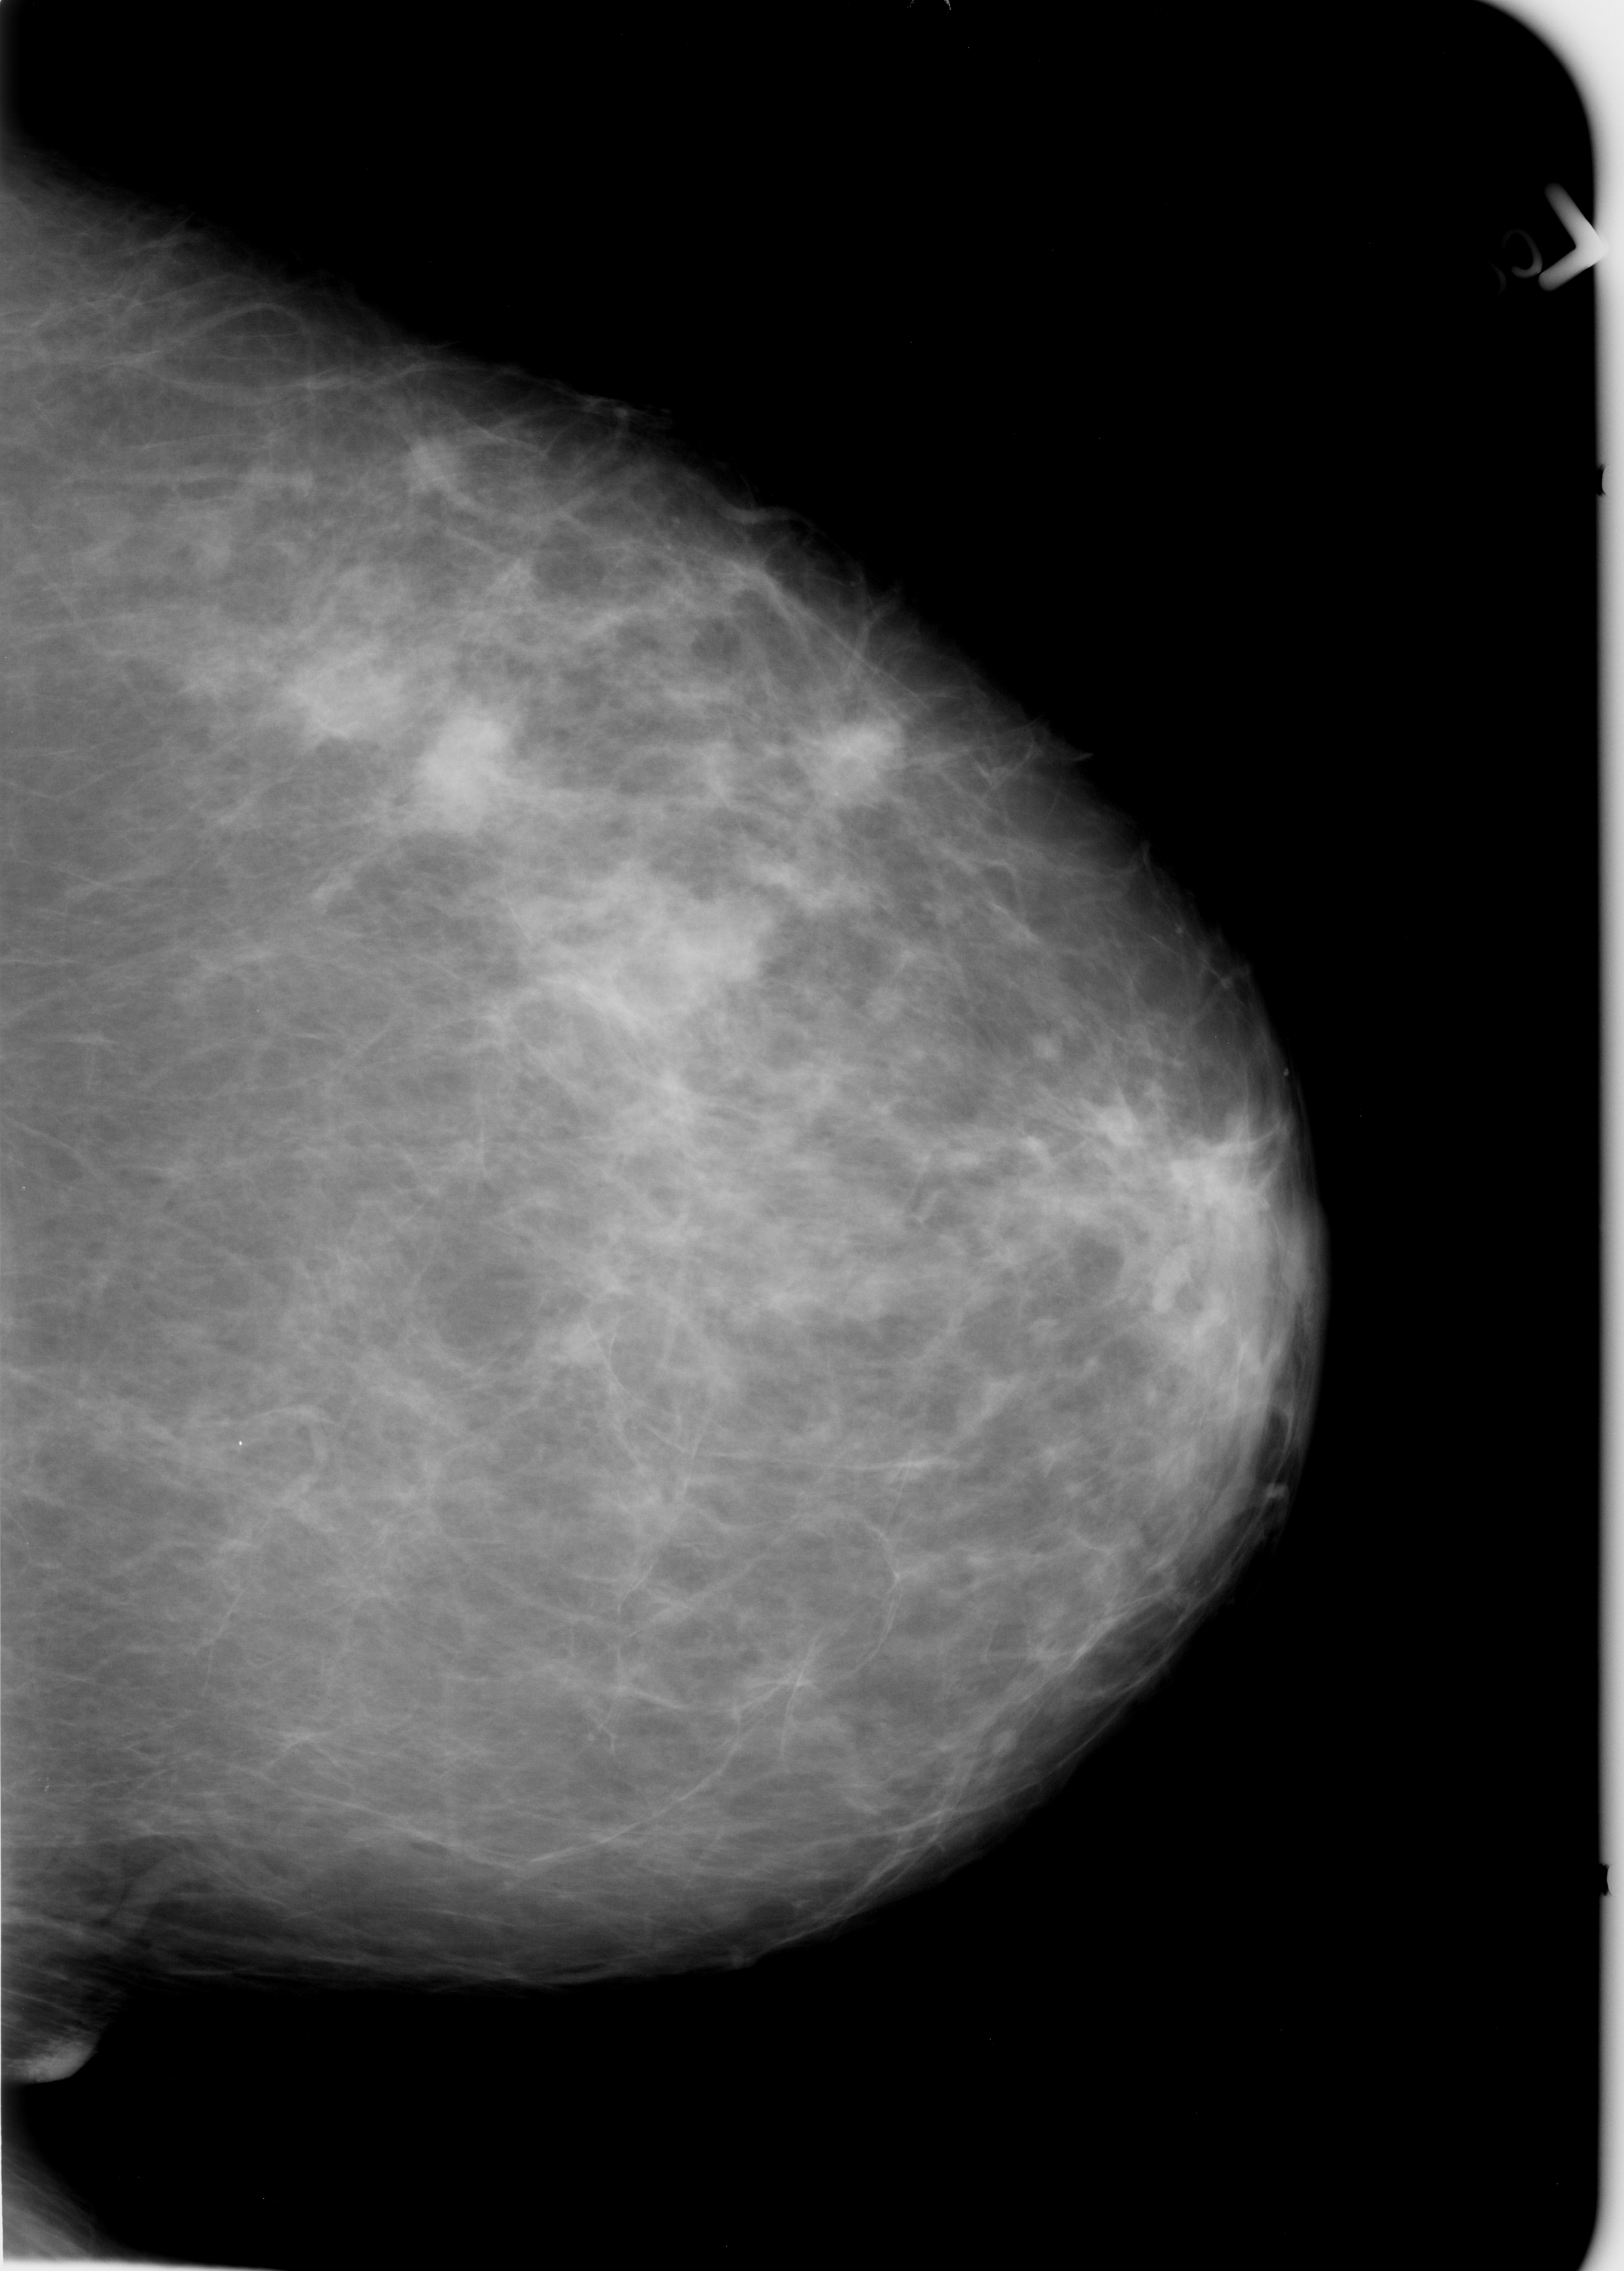
Digitized screen-film mammogram, left breast, craniocaudal (CC) view, breast composition: heterogeneously dense (BI-RADS density category 3 of 4).
Radiologist-marked abnormalities on this image: Finding 1 of 3: mass, shape lobulated, margins circumscribed / ill defined; BI-RADS assessment category 3; subtlety rating 3 on a 1 (subtle) to 5 (obvious) scale; pathology (as recorded): malignant. Finding 2 of 3: mass, shape lobulated, margins circumscribed / ill defined; BI-RADS assessment category 3; subtlety rating 3 on a 1 (subtle) to 5 (obvious) scale; pathology (as recorded): malignant. Finding 3 of 3: mass, shape lobulated, margins circumscribed / ill defined; BI-RADS assessment category 3; pathology (as recorded): malignant.